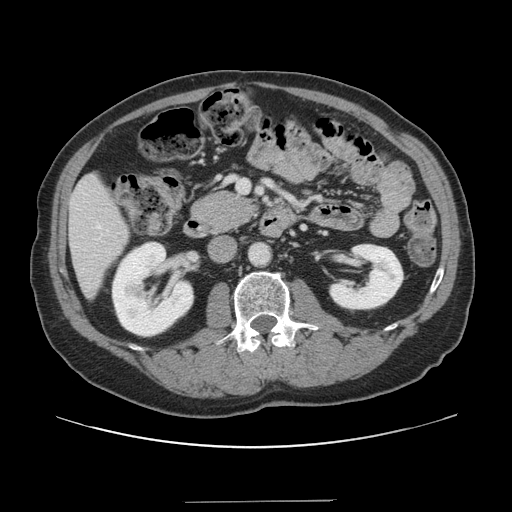
Contrast-enhanced abdominal CT, one axial slice. Slice 54 of 151 in the series (ordered by position). 120 kVp. Soft-tissue window (W 400 / L 40 HU). 512 × 512 image matrix, field of view 399 × 399 mm. Male patient, age 63 years. From the clinical record (not read from this slice): diagnosis: colorectal cancer liver metastases, imaged before liver resection; multiple liver metastases: no; largest metastasis: 2.1 cm; chemotherapy before resection: no.
Outlined on this slice (outlined manually by an expert reader):
- hepatic veins: bounding box (x1, y1, x2, y2) in pixels: (97, 226, 100, 228)
- liver: (70, 175, 129, 296)
- planned liver remnant (the part of the liver to remain after resection): (70, 175, 128, 295)
- portal vein (with intrahepatic branches): (238, 180, 248, 192)